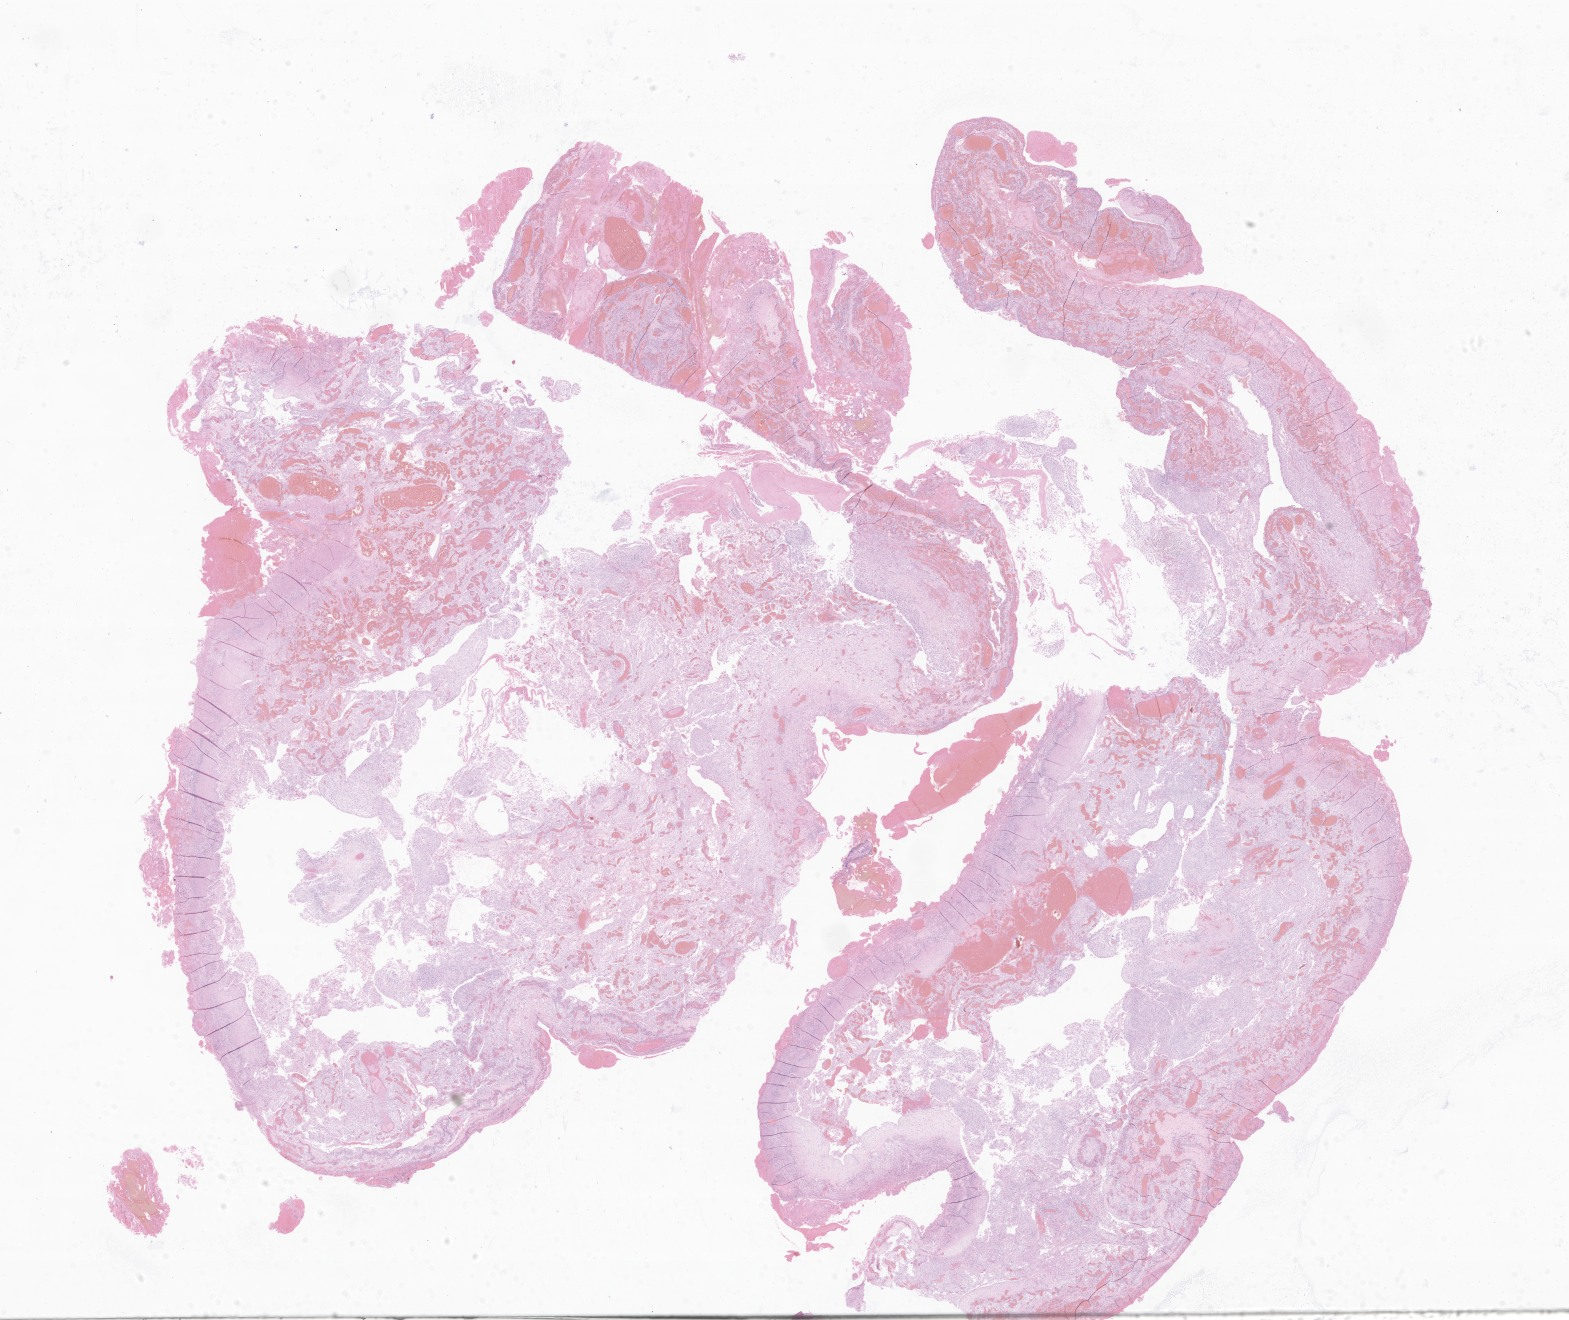
Whole-slide image, haematoxylin and eosin stain of tumor tissue from the brain, whole scanned area (about 26.5 x 22.3 mm) shown as a low-resolution overview, FFPE section. Patient: male, age 76 months.
Recorded diagnosis: Pilocytic astrocytoma.